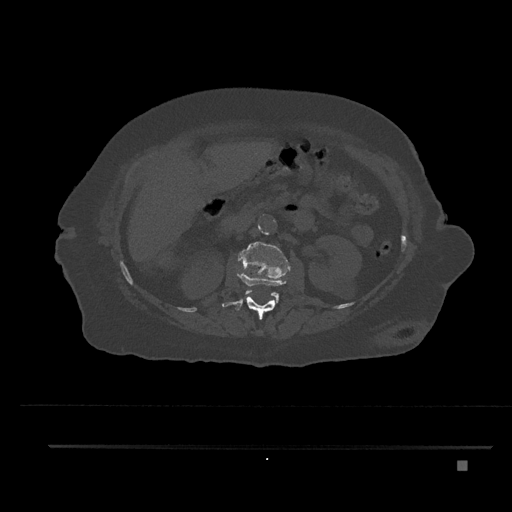
CT including the spine, one axial slice. Position 208 of 797 along the scan axis. Bone window (W 1800 / L 400 HU). 0.5 mm slice thickness. 512 × 512 image matrix, field of view 437 × 437 mm. Female patient, age 76 years. From the clinical record (not read from this slice): primary cancer: lung; vertebrae with lytic lesions (as recorded): T11, L3.
Outlined on this slice (semi-automatically segmented with operator editing):
- L1 vertebra: bounding box (x1, y1, x2, y2) in pixels: (222, 272, 288, 320)
- L2 vertebra: (238, 242, 291, 303)